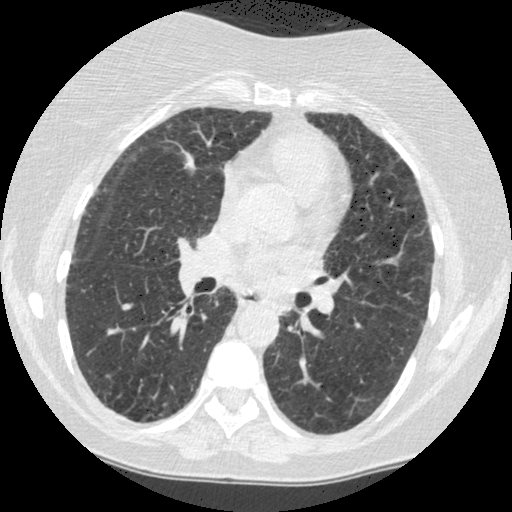
Axial slice from a low-dose chest CT screening exam. Baseline screening round. Lung window (W 1500 / L -600 HU). 1.25 mm slice thickness. Slice 212 of 442 in the series. Female, age 60 years at enrolment. Former smoker at enrolment.
• Expert-annotated lung lesion, bounding box (x1, y1, x2, y2) in pixels: (263, 288, 306, 329).
• The screening reader recorded 2 non-calcified nodules or masses ≥4 mm on this exam (right lower lobe, left lower lobe); which of them this box marks is not recorded.
• Later outcome: lung cancer diagnosed 794 days after this screen — small cell carcinoma, NOS, left lower lobe, undifferentiated (G4), stage IV (AJCC 6th edition), 69 mm at pathology.